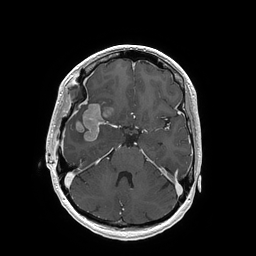
Brain MRI from a brain-tumour surgery series, one axial slice; T1-weighted post-contrast; 1 mm slice thickness; 256 × 256 image matrix, field of view 250 × 250 mm. Case-level facts recorded for this patient, not image findings: histopathology: Glioblastoma; WHO grade: 4; IDH mutation: no.
Annotated regions visible in this slice (manually delineated by an expert):
- tumour: bounding box [x1, y1, x2, y2] px = [75, 104, 112, 142]